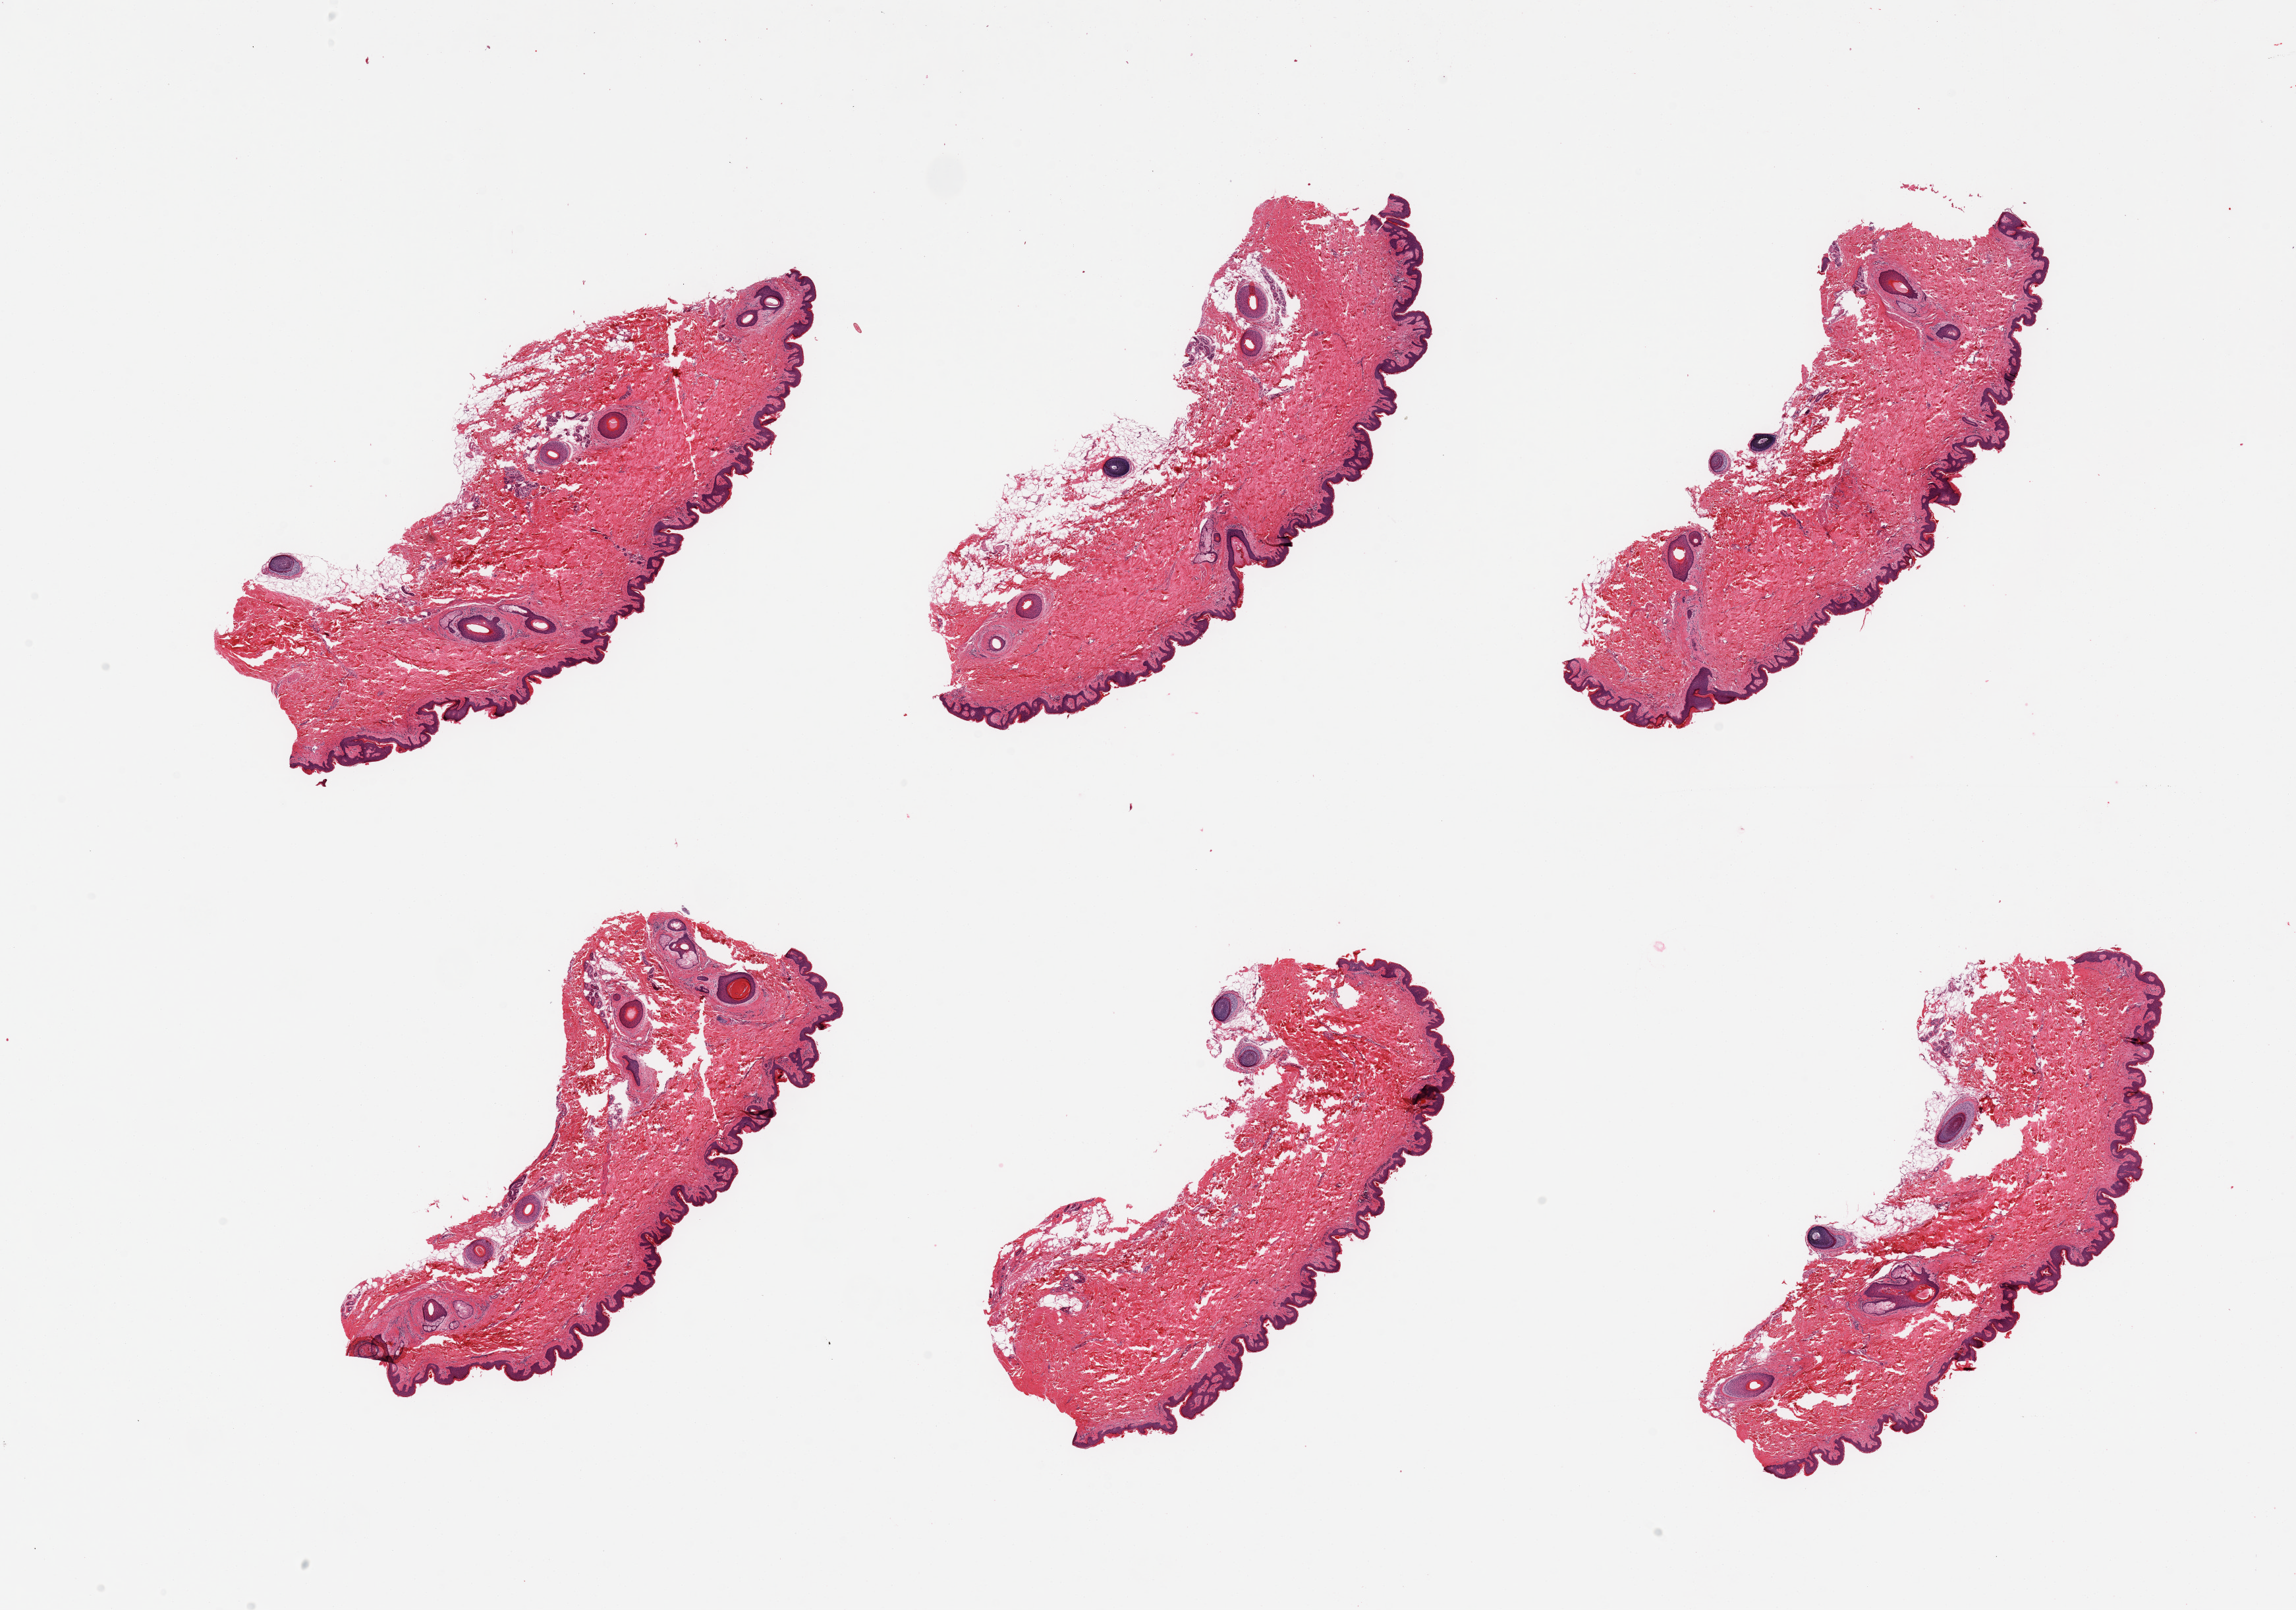
Whole-slide image, haematoxylin and eosin stain — a low-resolution overview of the entire scanned area, about 27.6 x 19.3 mm (from a 20x scan); PAXgene-fixed, paraffin-embedded tissue; section of skin of suprapubic region (target tissue); donor tissue sample. Male donor.
* pathologist's review note for this sample: 6 pieces, focal dermal fat up to ~0.6mm